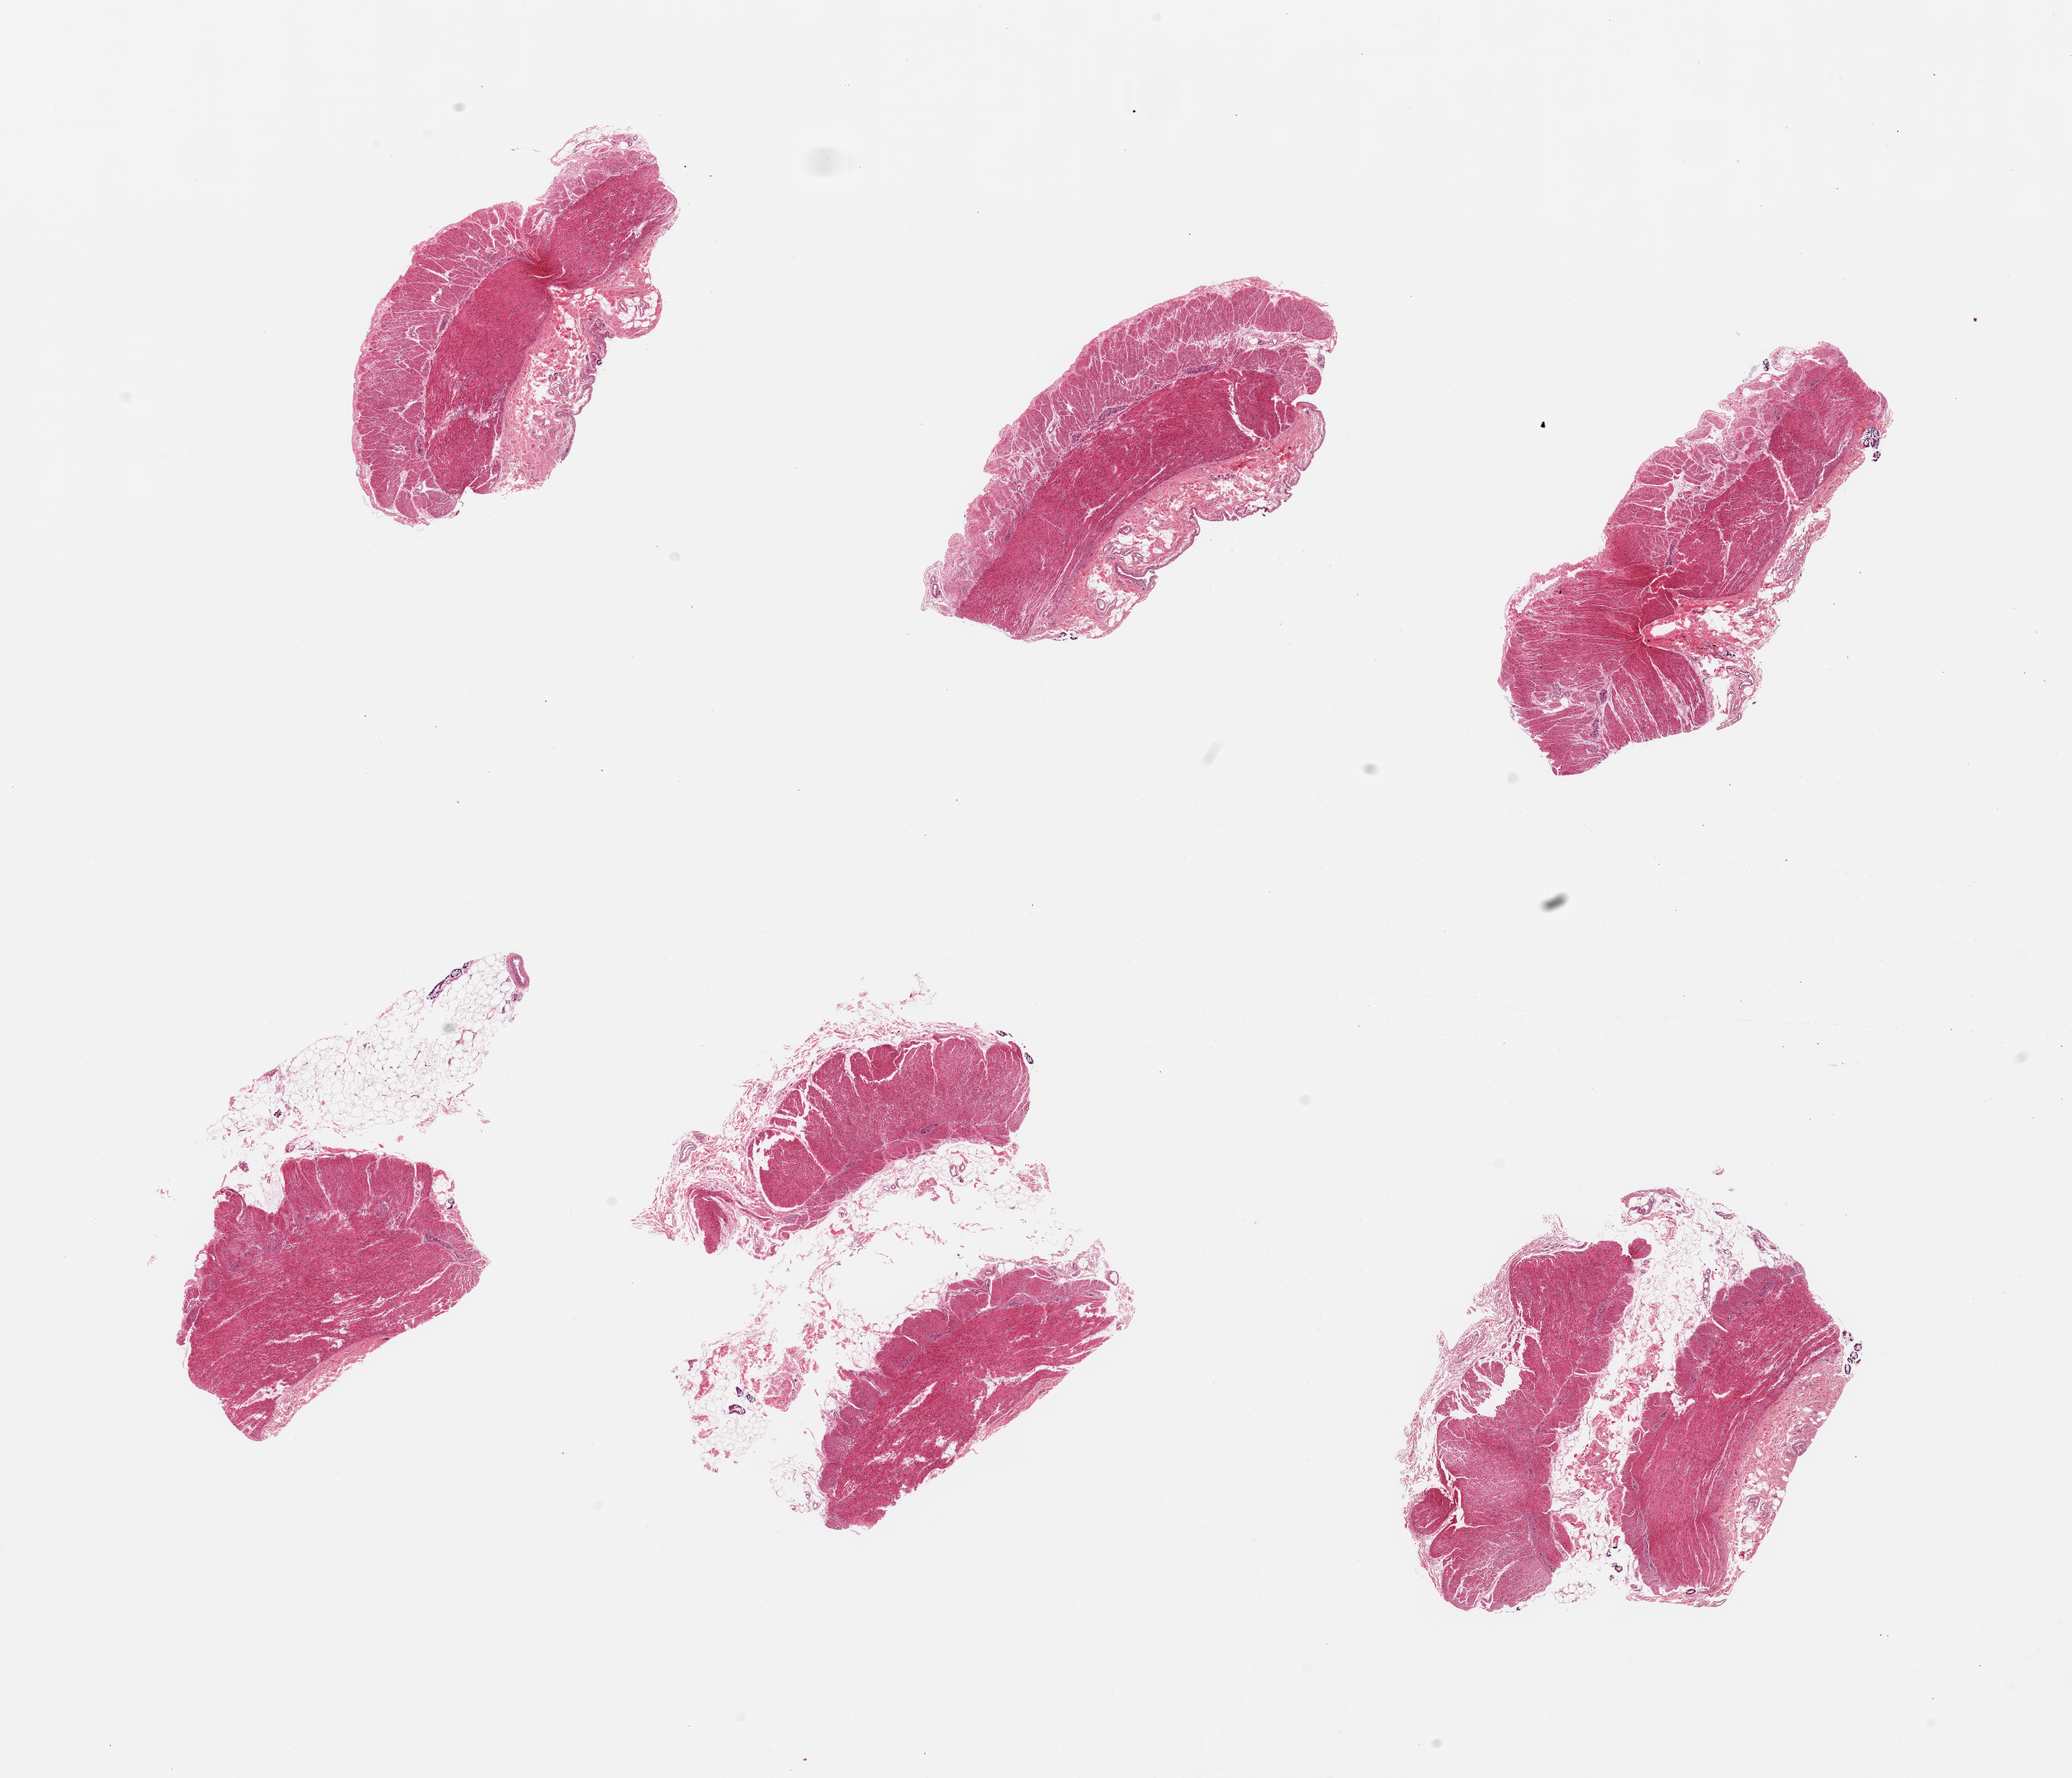
Digitized haematoxylin and eosin-stained section, brightfield, low-resolution overview of the scanned area, about 21.7 x 18.6 mm (acquisition: 20x scan), PAXgene-fixed paraffin-embedded (PFPE) section, section of sigmoid colon (target tissue), tissue donor sample.
Pathologist's review note for this sample: 6 pieces; 3 have extraneous fat.